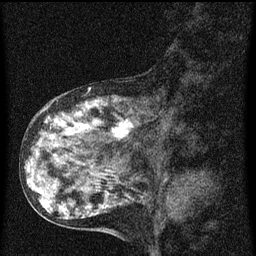
Breast MRI (dynamic contrast-enhanced), one sagittal slice; slice 25 of 60 in the series (ordered by position); dynamic contrast-enhanced series, image 2 of 3 at this slice position (ordered by acquisition); 1.5 T; TE 4.2 ms, TR 8 ms; 2 mm slice thickness; 256 × 256 image matrix, field of view 180 × 180 mm. Female patient, age 55 years.
Annotated regions visible in this slice (semi-automatic segmentation, software-assisted and operator-edited):
- analysis volume of interest (the breast-tissue region the enhancement analysis was run in; not a lesion): bounding box <38,92,167,159> (left, top, right, bottom; pixels)
- tumour enhancement mask (voxels above the 70 % enhancement threshold inside the analysis volume of interest): <46,118,135,141>